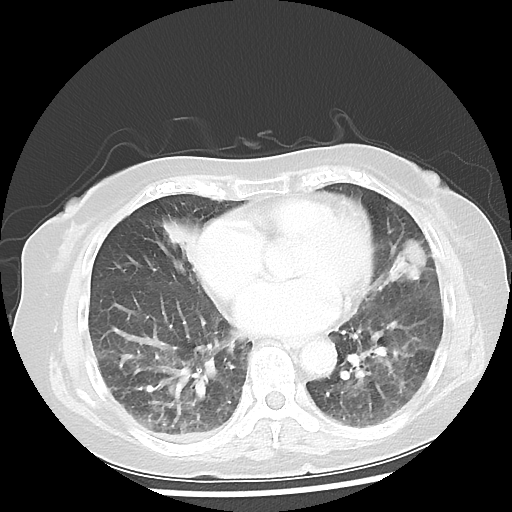
Chest CT, one axial slice. Slice 19 of 50 in the series (ordered by position). Reconstruction kernel LUNG. 100 kVp. Lung window (W 1500 / L -600 HU). 512 × 512 image matrix, field of view 332 × 332 mm. Patient: female, 77 years. From the clinical record (not read from this slice): clinical TNM (as recorded): T2 N3 M1a.
Annotated regions visible in this slice (bounding box drawn by a radiologist):
- lung tumour (recorded histology: adenocarcinoma): box from (x=390, y=234) to (x=430, y=294) px